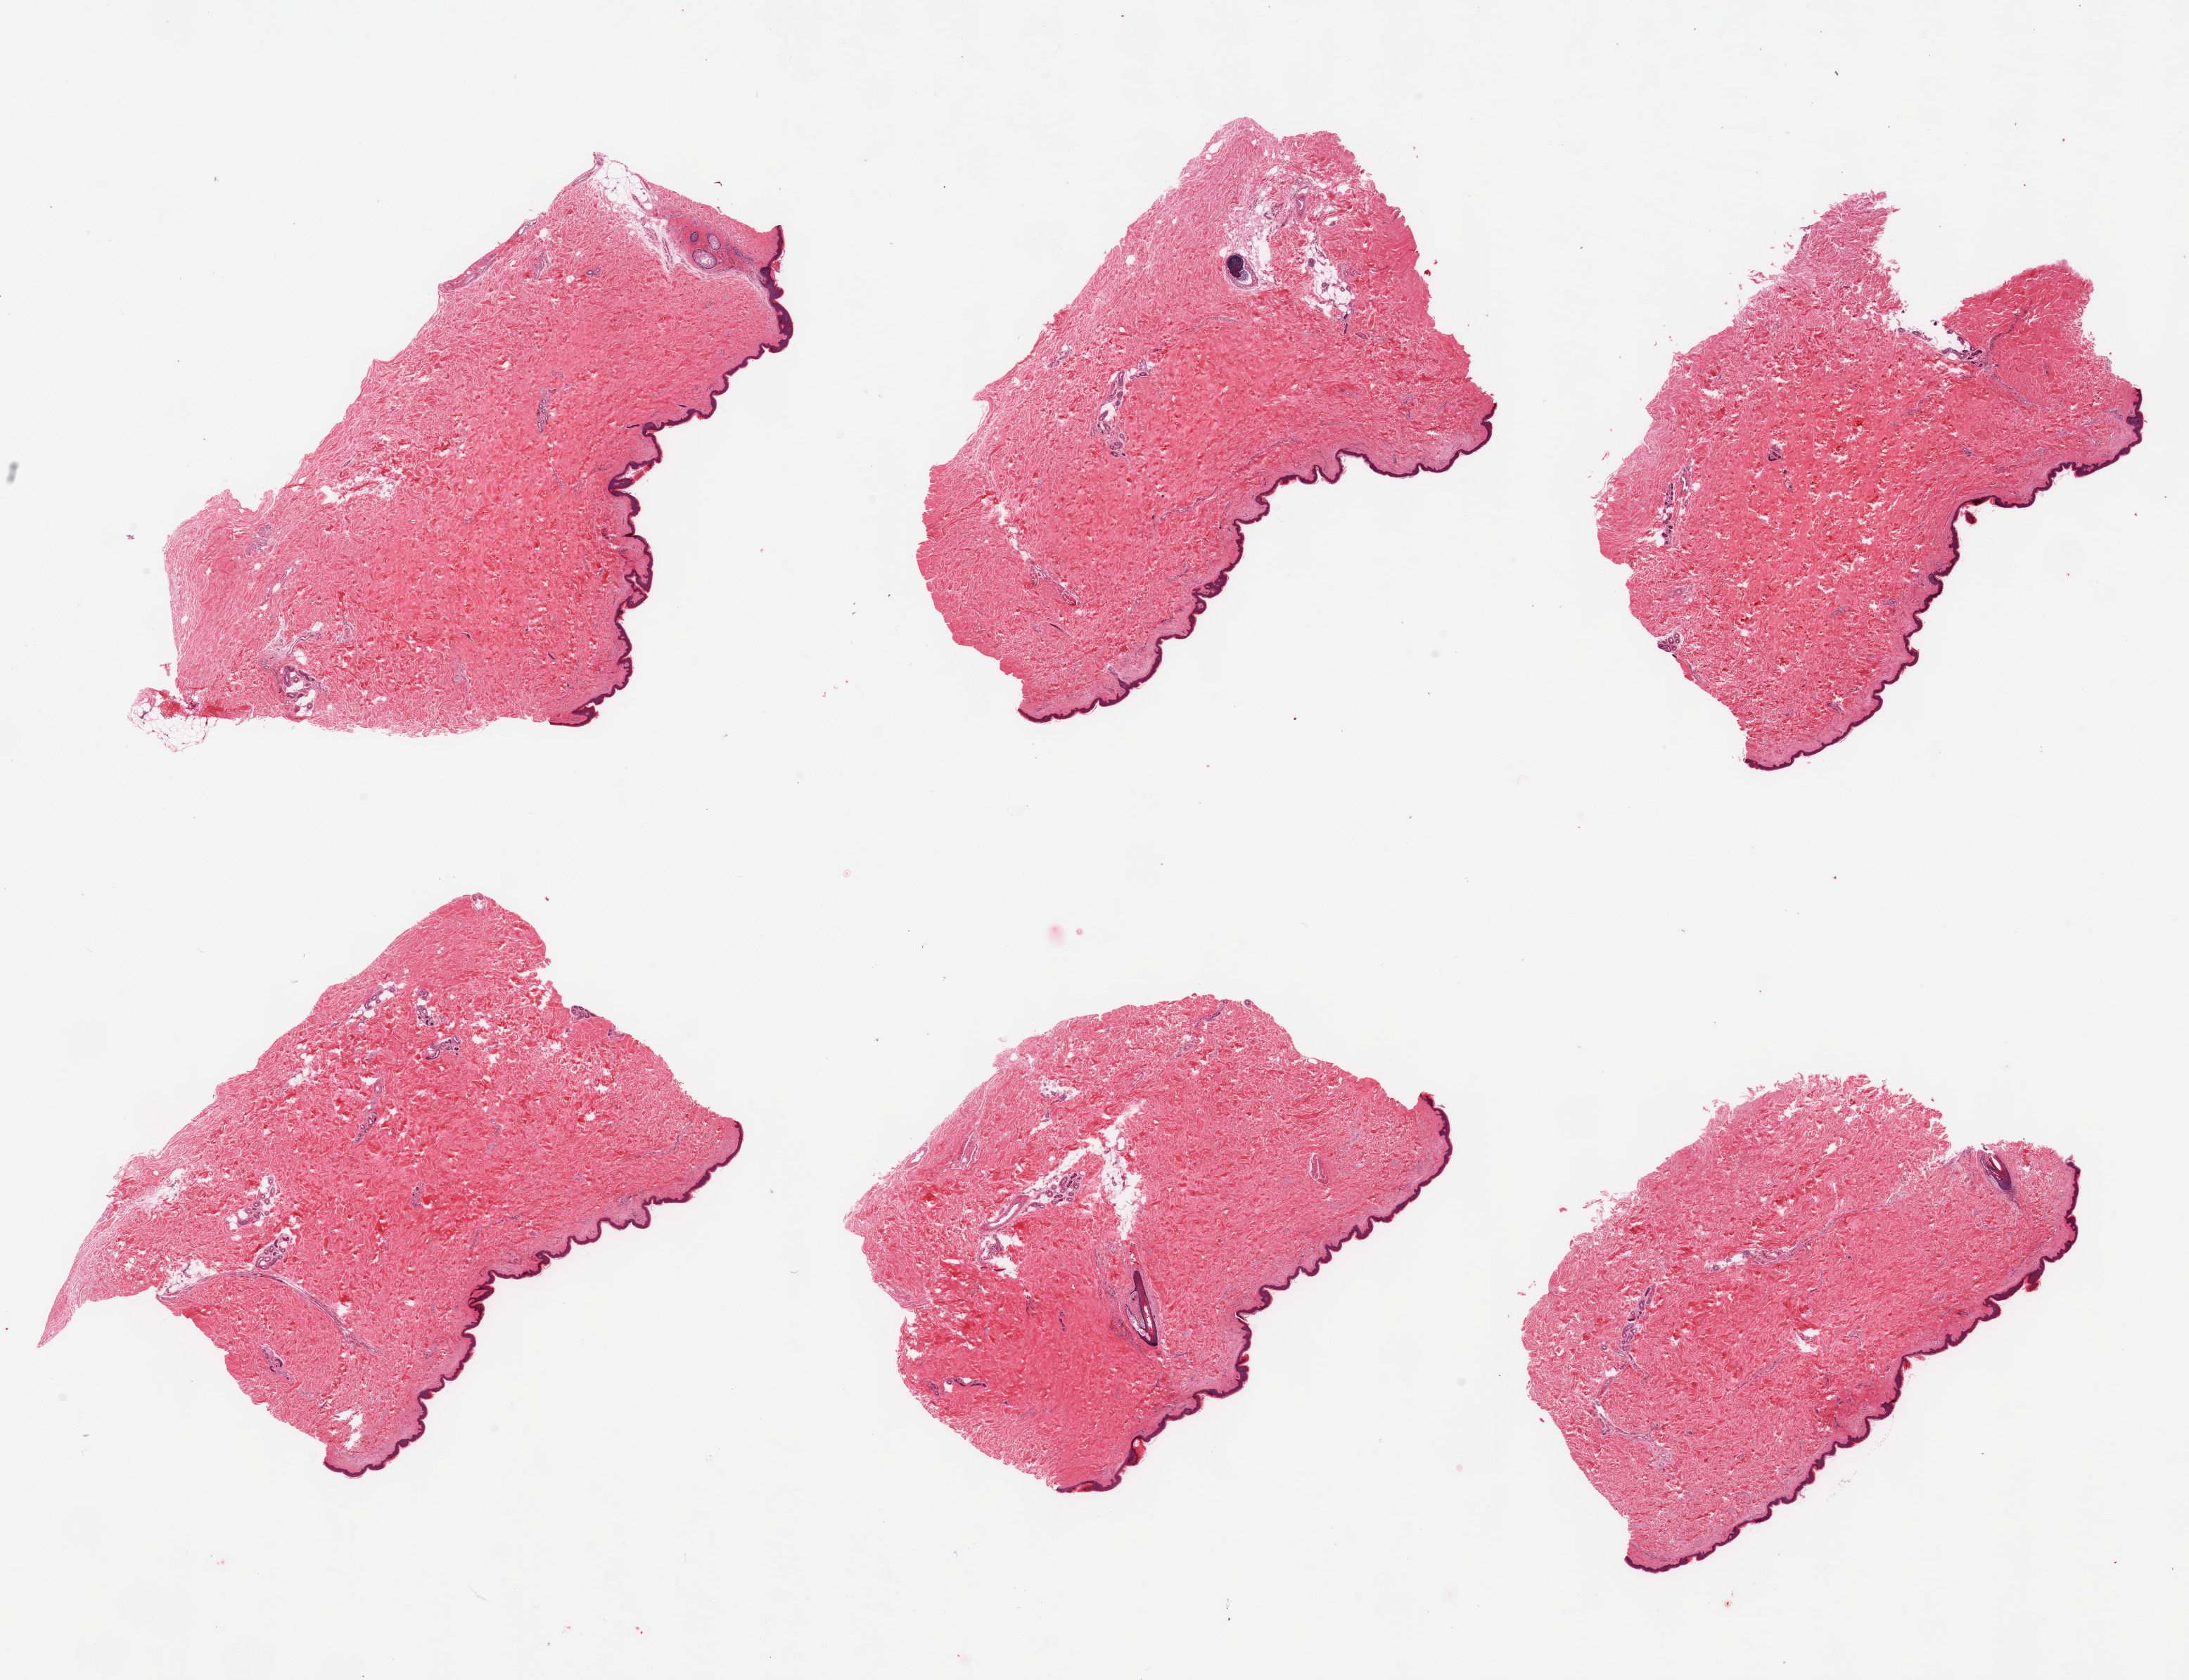
Hematoxylin and eosin (H&E) whole-slide image, brightfield, whole scanned area (about 24.6 x 18.9 mm, slide scanned at 20x) shown as a low-resolution overview; PAXgene-fixed, paraffin-embedded tissue; section of skin of suprapubic region (target tissue); tissue donor sample. Donor: male.
• pathologist's review note for this sample: 6 pieces, minimal dermal fat; squamous epithelium is ~35 microns